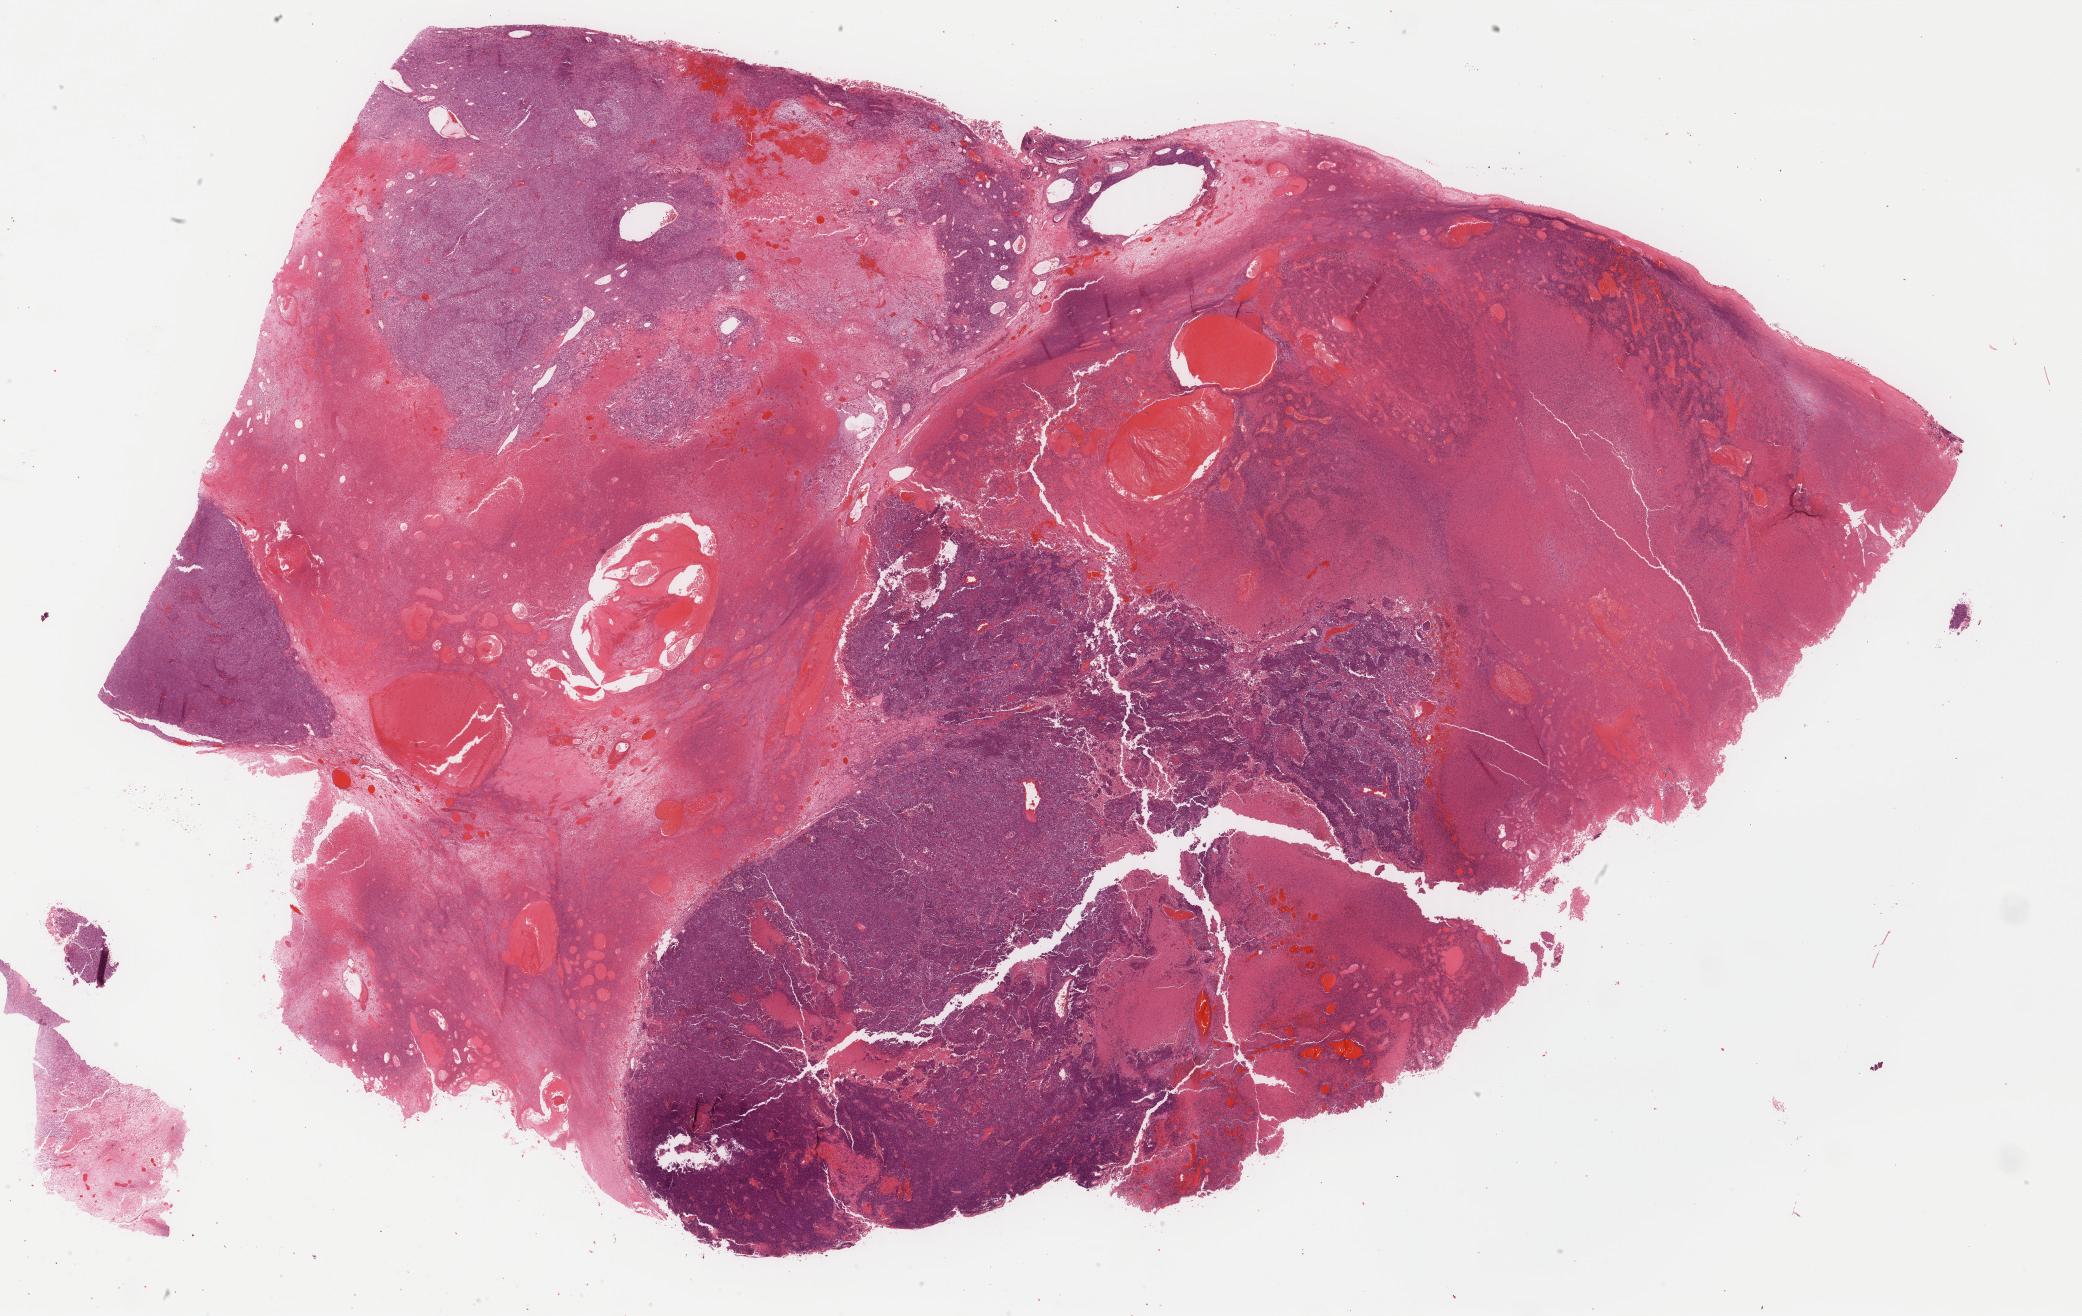
Whole-slide histology image, H&E-stained, low-resolution overview of the scanned area, about 33.1 x 20.9 mm (acquisition: 40x scan); formalin-fixed paraffin-embedded (FFPE) diagnostic section; sample: primary tumour, uterus. Female, age 72 years at initial diagnosis.
FIGO stage: IVB. Histologic diagnosis: Mullerian mixed tumor.